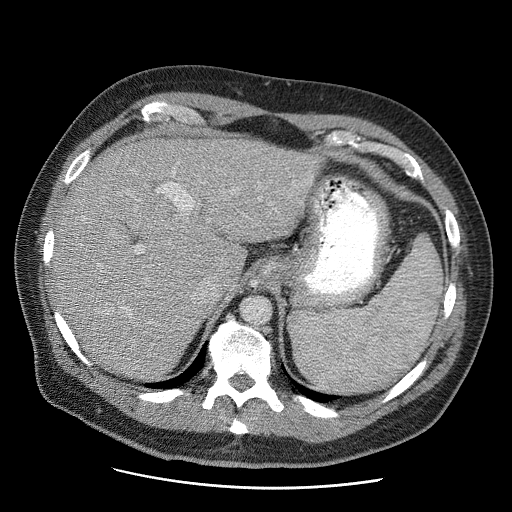
Contrast-enhanced abdominal CT (liver protocol), one axial slice; position 40 of 81 along the scan axis; soft-tissue window (W 400 / L 40 HU); 2.5 mm slice thickness; 512 × 512 image matrix, field of view 380 × 380 mm. From the clinical record (not read from this slice): diagnosis: hepatocellular carcinoma (patient treated with transarterial chemoembolisation; whether this scan precedes or follows treatment is not stated here); TNM stage (as recorded): Stage-IIIA.
Structures marked on this image (semi-automatically segmented with operator editing):
- liver parenchyma outside the tumour (the mass and vessels are separate outlines, so this box may not span the whole liver): bounding box <52,134,320,380> (left, top, right, bottom; pixels)
- liver vessels: <125,182,193,310>